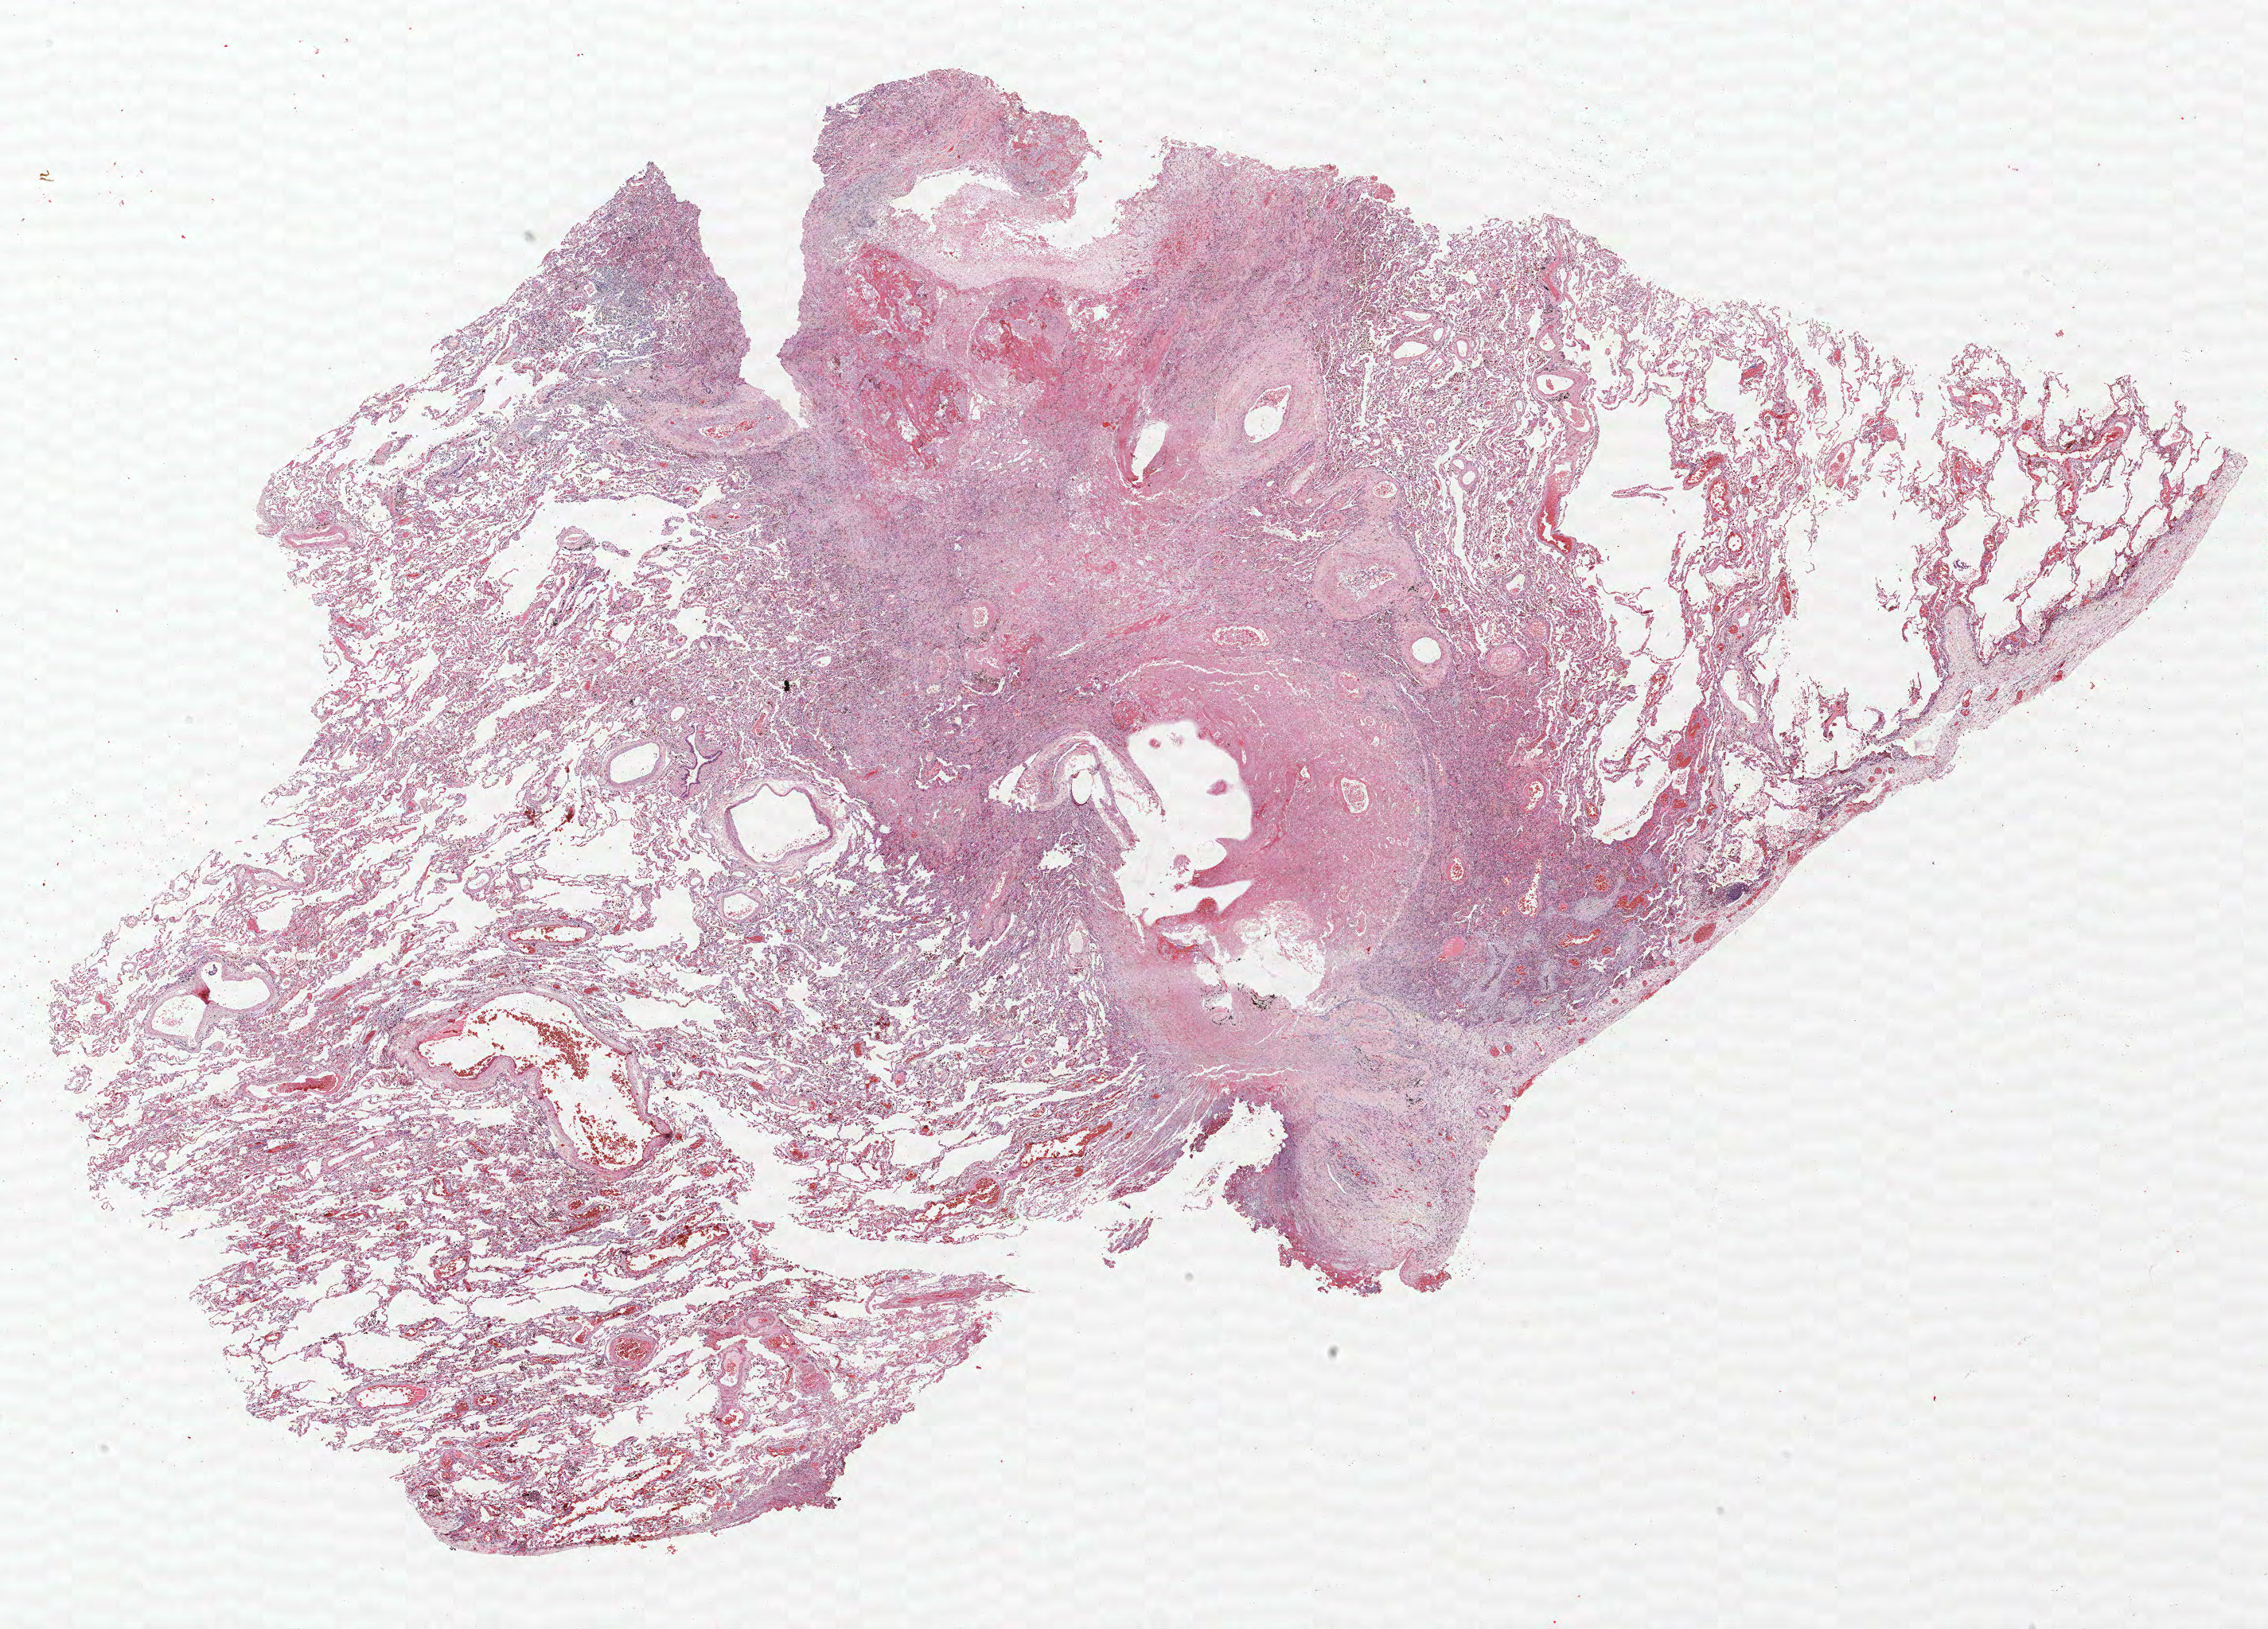
H&E-stained whole-slide image — shown as a low-resolution overview of the whole scanned area (about 22.8 x 16.4 mm, acquisition: 40x scan), formalin-fixed paraffin-embedded (FFPE) section, lung tissue. Male patient, aged 64 at enrolment. Former smoker at enrolment. Grade: poorly differentiated (G3).
* primary tumour location (clinical record): left upper lobe
* stage (AJCC 6th edition): IA
* tumour size (pathology): 10 mm
* participant's lung-cancer diagnosis: Adenocarcinoma, NOS (ICD-O-3 8140/3)